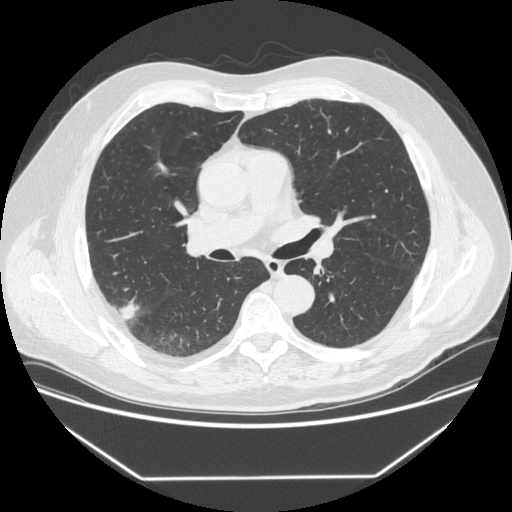
Chest CT (low-dose screening protocol), one axial image. First (baseline) screen. Lung window (W 1500 / L -600 HU). 1.25 mm slice thickness. Standard (soft-tissue) reconstruction kernel (STANDARD). 120 kVp. Slice 209 of 342 in the series. 512 × 512 image matrix. Male participant, aged 64 years at enrolment.
- Expert reader's lesion annotation, bounding box <101,298,142,329> (left, top, right, bottom; pixels).
- Reader record for this screening exam (exam-level; its link to the box is not recorded): non-calcified nodule or mass ≥4 mm, right upper lobe, 12 × 12 mm, smooth margins, soft tissue attenuation.
- Official screen result: positive, change unspecified: nodule(s) >= 4 mm or enlarging nodule(s), mass(es), or other non-specific abnormalities suspicious for lung cancer.
- Participant outcome: lung cancer diagnosed 92 days after this screen — adenocarcinoma, NOS, right upper lobe, poorly differentiated (G3), stage IIIB (AJCC 6th edition), 15 mm at pathology.